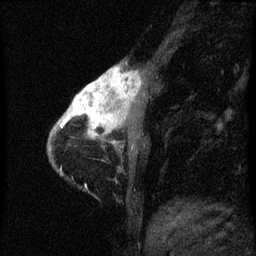
Breast MRI (dynamic contrast-enhanced), one sagittal slice; dynamic contrast-enhanced series, image 2 of 3 at this slice position (ordered by acquisition); 1.5 T; TE 4.2 ms, TR 8 ms; 2 mm slice thickness; 256 × 256 image matrix. Female patient, age 38 years.
Structures marked on this image (semi-automatic segmentation, software-assisted and operator-edited):
- analysis volume of interest (the breast-tissue region the enhancement analysis was run in; not a lesion): bounding box <61,62,141,147> (left, top, right, bottom; pixels)
- tumour enhancement mask (voxels above the 70 % enhancement threshold inside the analysis volume of interest): <61,68,140,143>